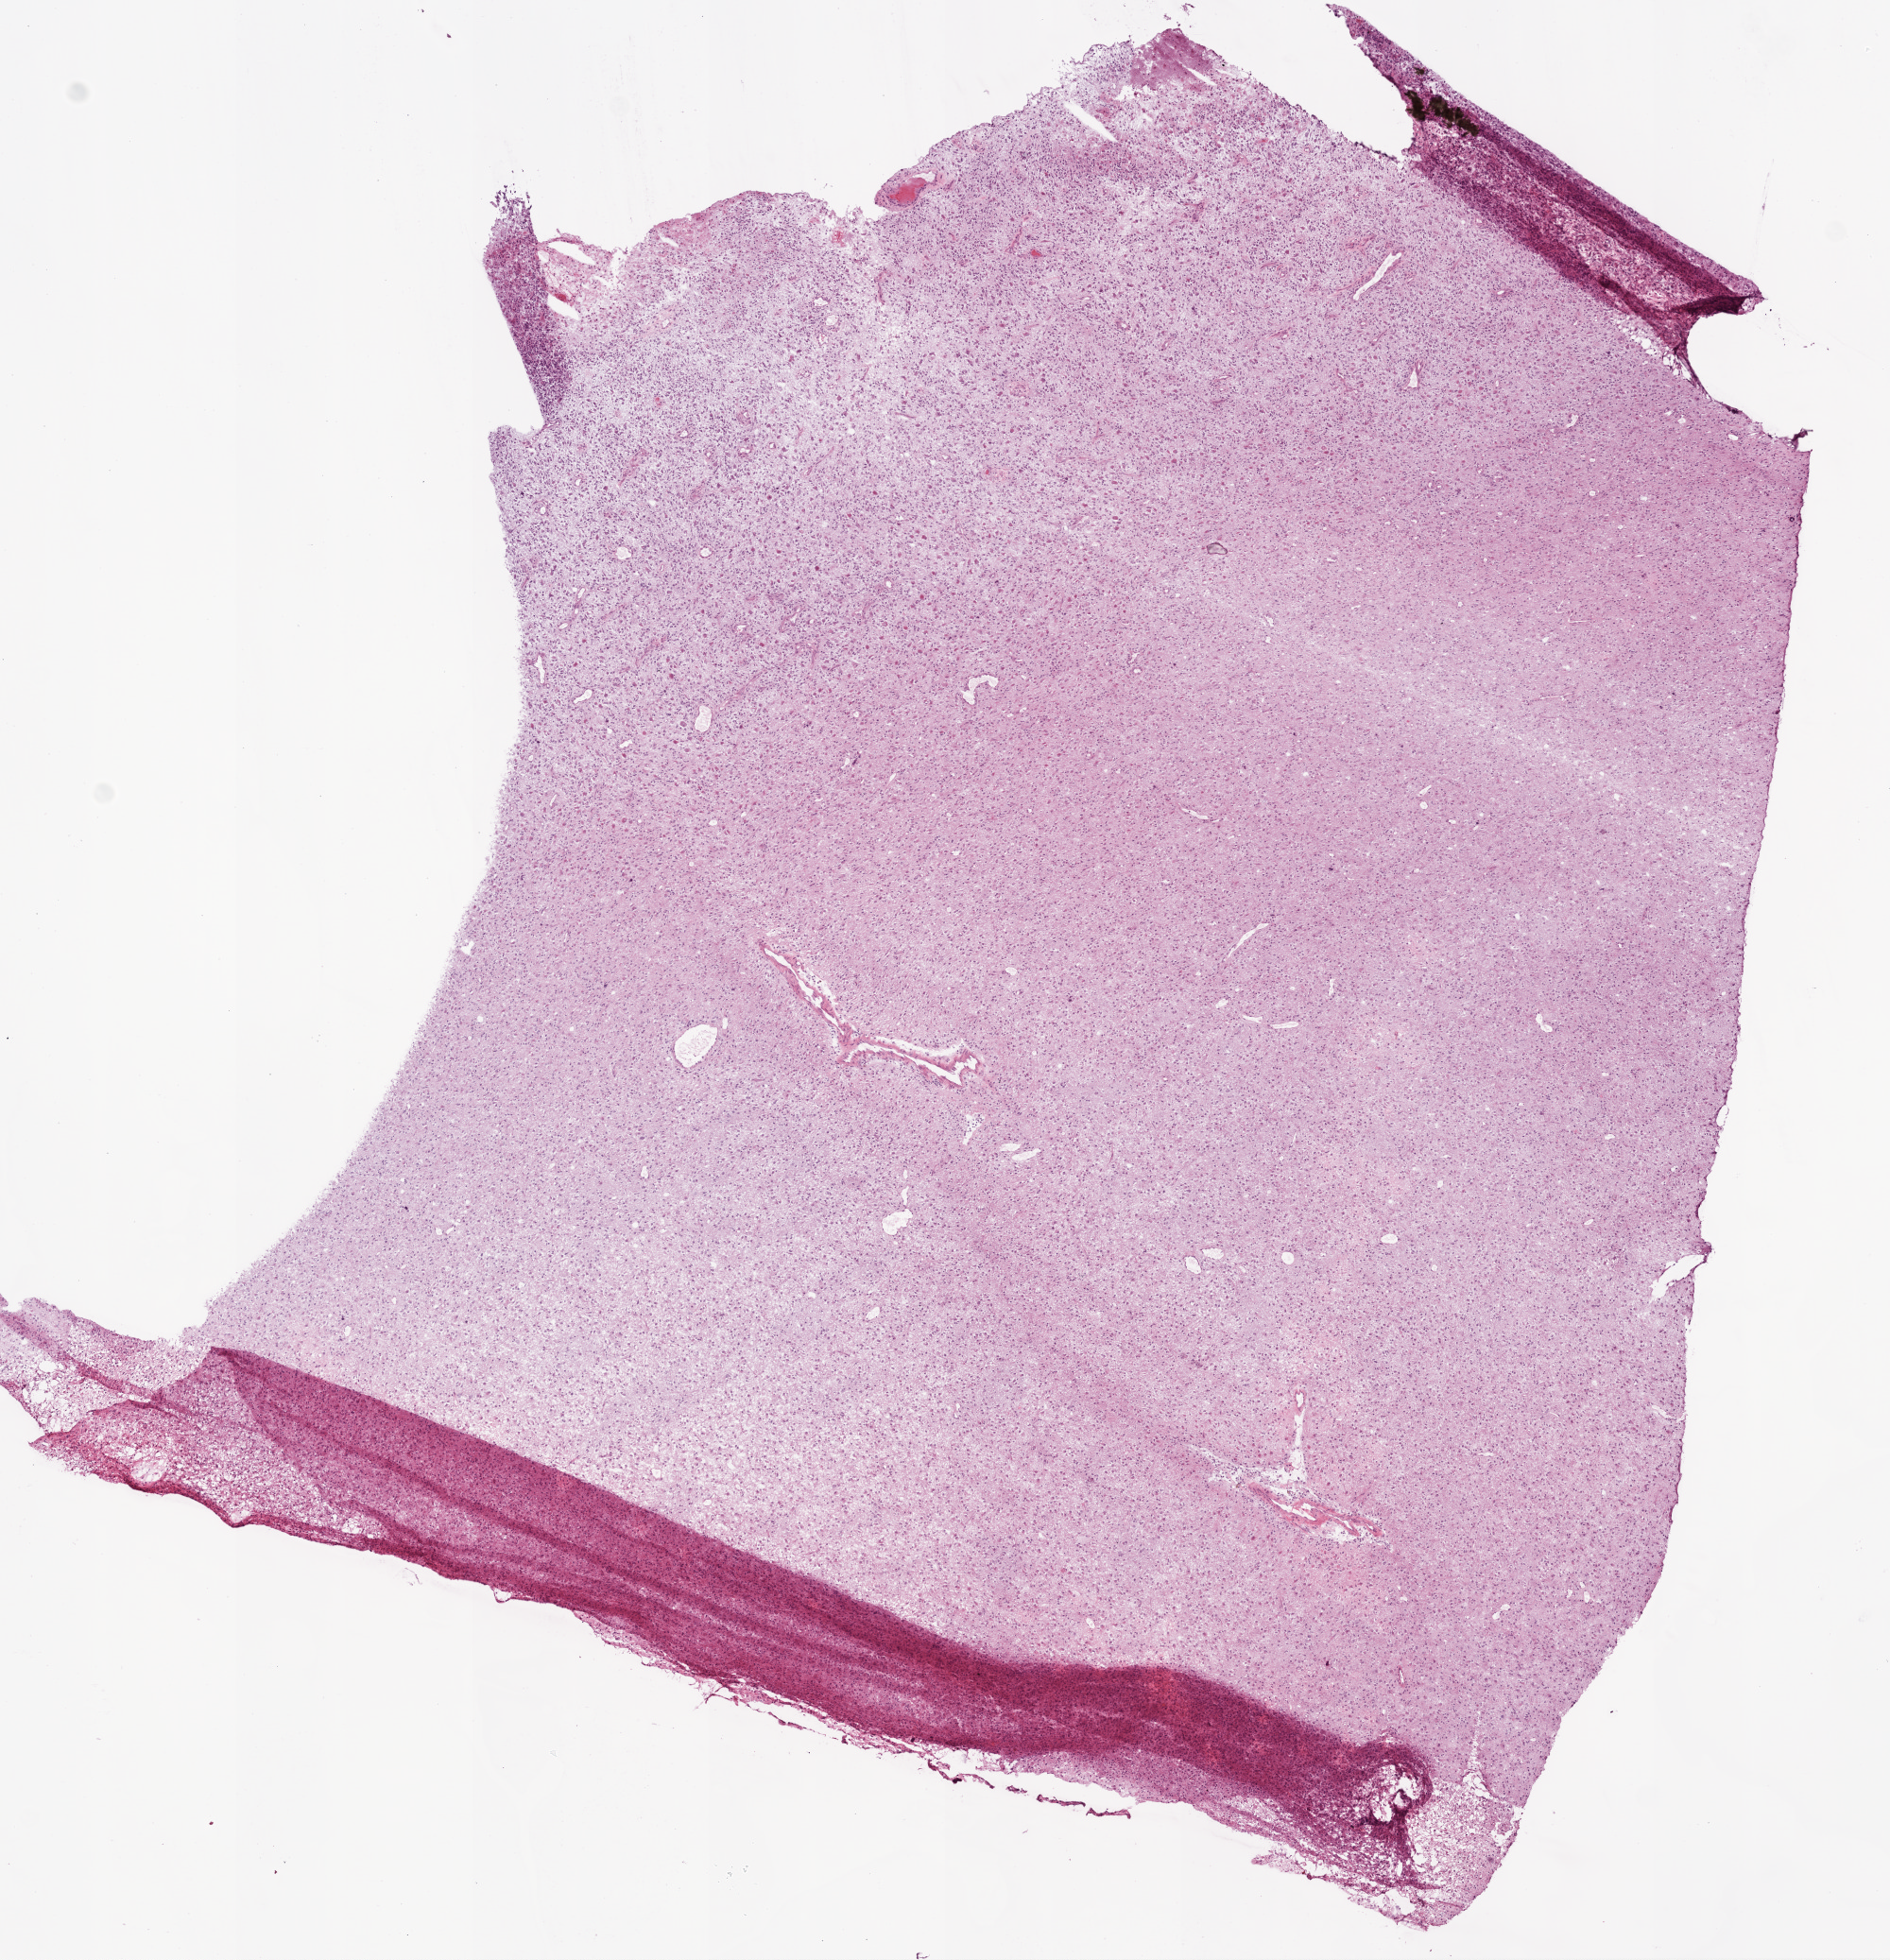
H&E whole-slide image — low-resolution overview of the scanned area, about 8.0 x 8.3 mm, frozen section from the bottom of the tissue portion, primary tumour sample from the brain. Patient: female, age at initial diagnosis 47 years. Pathologist review of this section (percent, as recorded): tumour cells 90%, tumour nuclei 80%.
Histologic diagnosis: Glioblastoma.